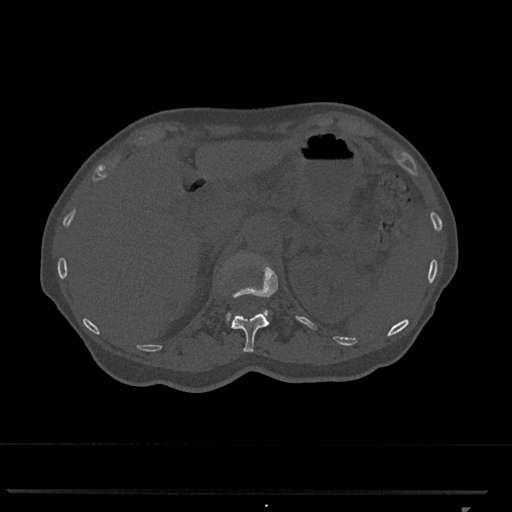
CT including the spine, one axial slice; slice 444 of 793 in the series (ordered by position); reconstruction kernel Br40s/3; 120 kVp; bone window (W 1800 / L 400 HU); 0.5 mm slice thickness; 512 × 512 image matrix, field of view 380 × 380 mm. Female patient, age 62 years. From the clinical record (not read from this slice): primary cancer: renal.
Annotated regions visible in this slice (semi-automatically segmented with operator editing):
- L1 vertebra: box from (x=226, y=255) to (x=268, y=321) px
- T12 vertebra: (x=227, y=255)–(x=278, y=352)